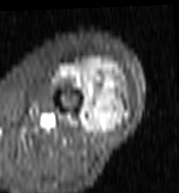
MRI of an extremity soft-tissue mass, one axial slice. Slice 41 of 103 in the series (ordered by position). STIR. MR volume resampled by the dataset authors to the PET/CT grid (not the native acquisition matrix). 3.27 mm slice thickness. 179 × 193 image matrix, field of view 175 × 188 mm. Female patient. From the clinical record (not read from this slice): histological type: undifferentiated – high grade; grade: high; site of the primary tumour: left thigh.
Annotated regions visible in this slice (expert contour drawn on MRI and transferred to this co-registered scan by the dataset authors):
- gross tumour volume including surrounding oedema: bounding box [x1, y1, x2, y2] px = [57, 57, 126, 134]
- gross tumour volume (mass): [82, 64, 126, 134]